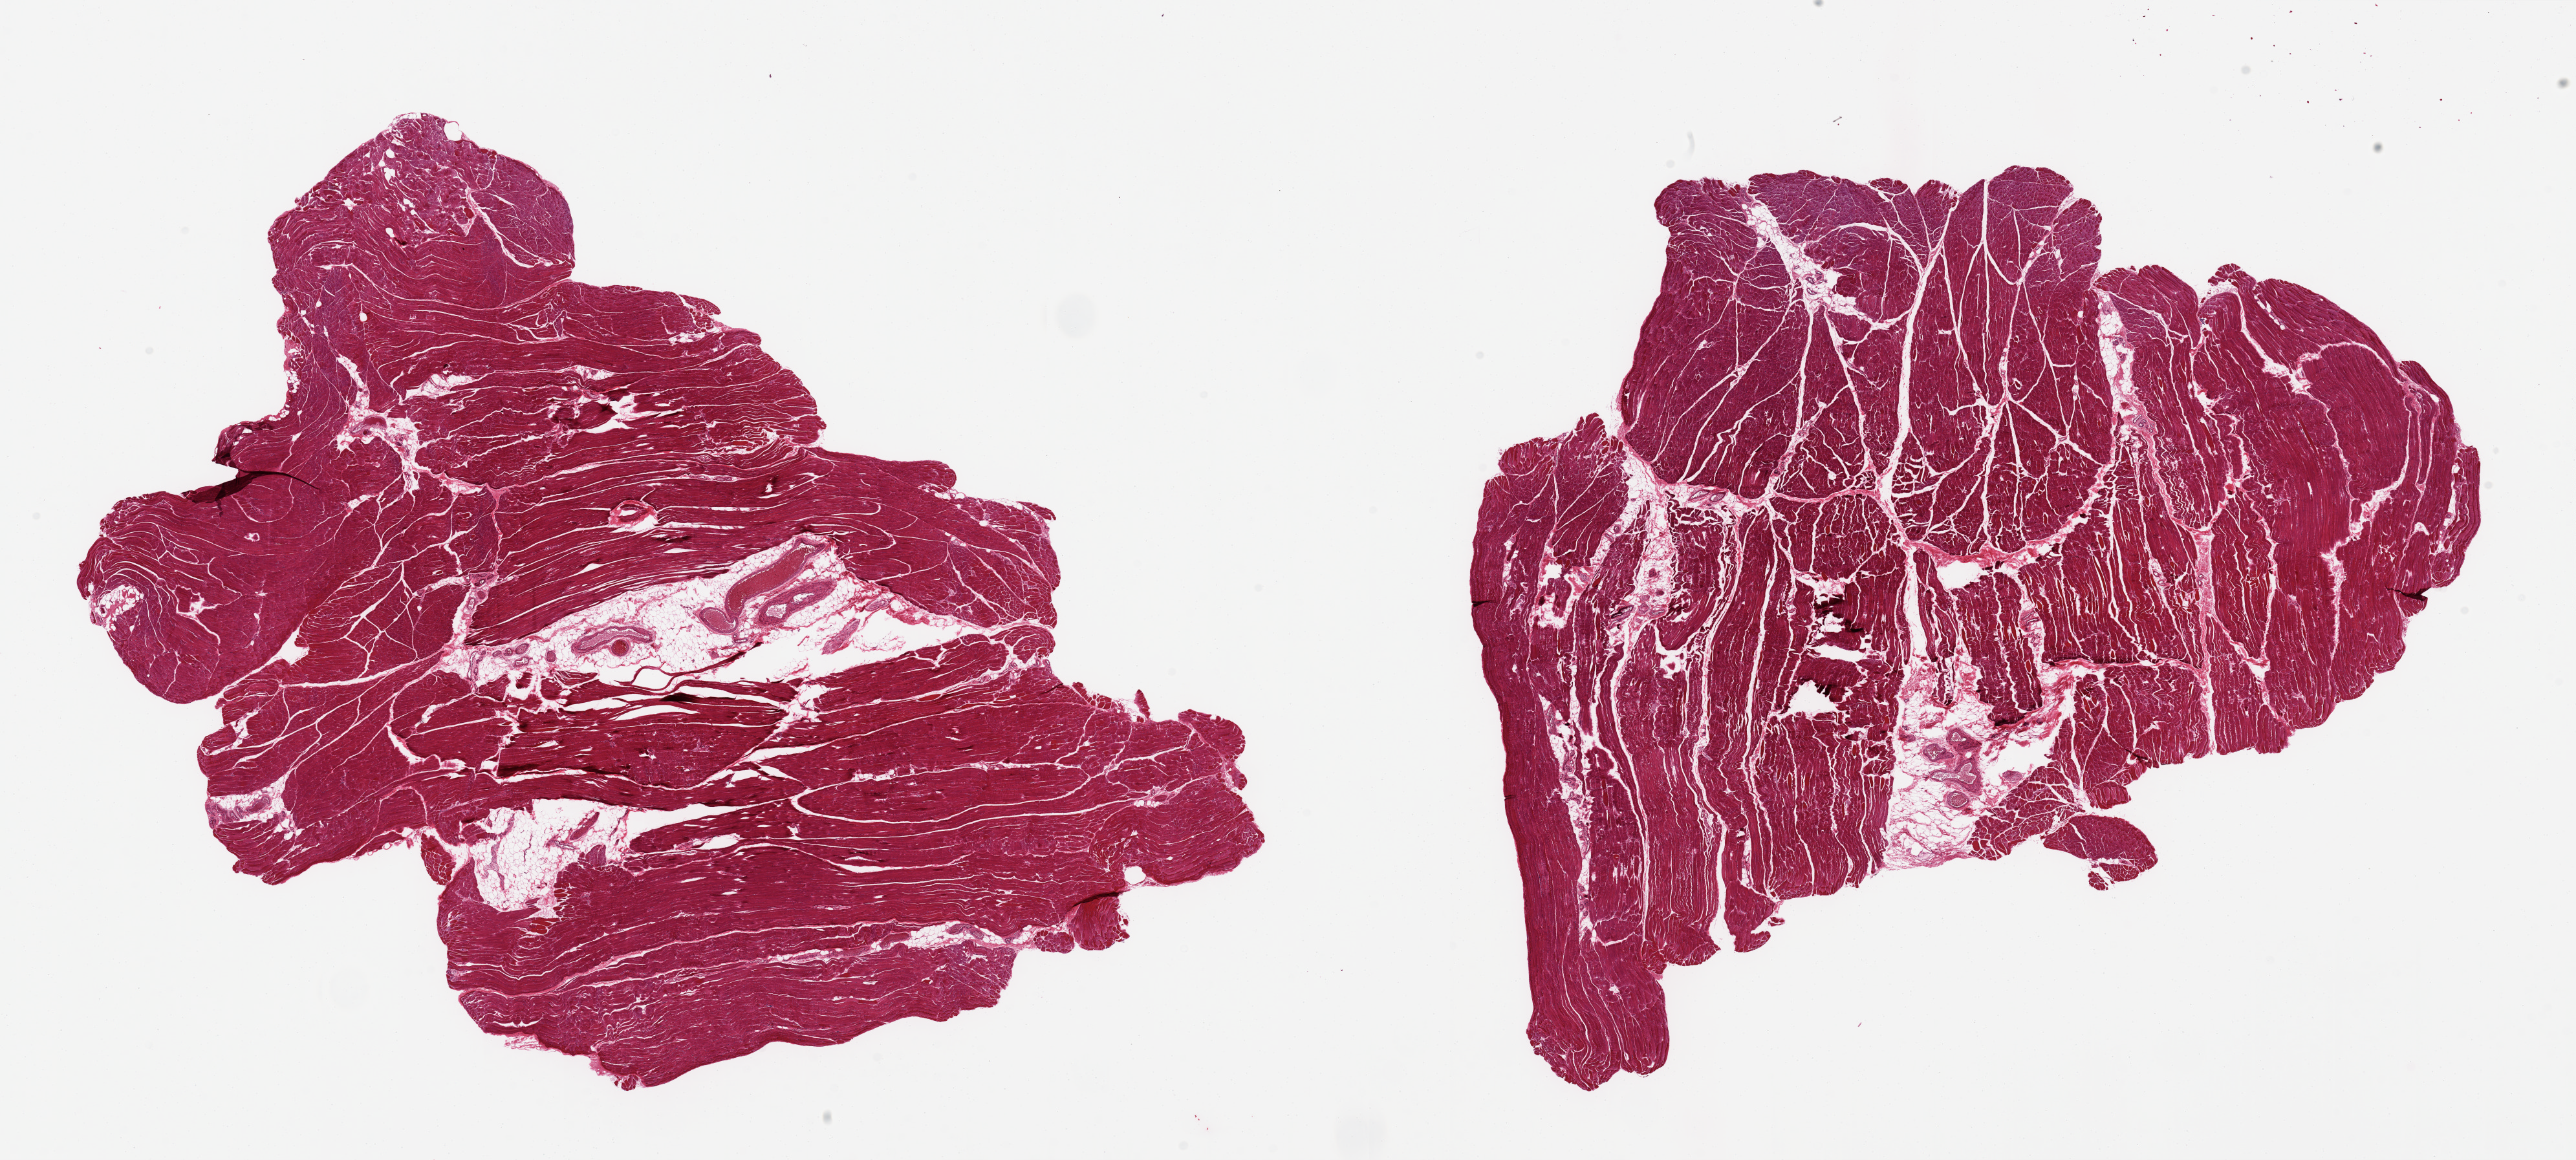
Whole-slide image, hematoxylin and eosin (H&E) stain, shown as a low-resolution overview of the whole scanned area (about 31.5 x 14.2 mm, acquisition: 20x scan); PAXgene-fixed, paraffin-embedded tissue; target tissue: skeletal muscle; donor tissue sample. Donor sex: male.
Review note (as recorded): 2 pieces; 10 & 20% internal fat.